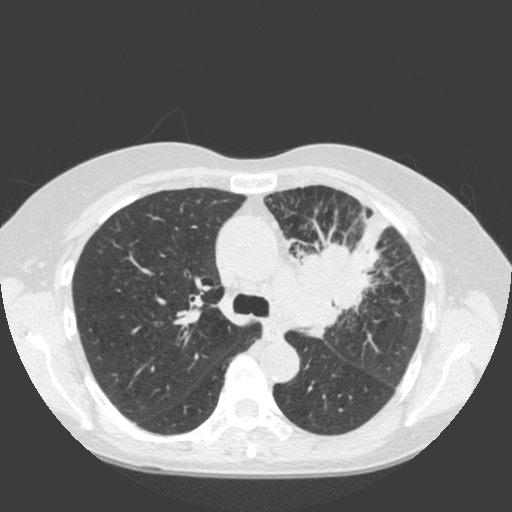
Low-dose screening chest CT, axial slice. First (baseline) screen. Lung window (W 1500 / L -600 HU). 2 mm slice thickness. Standard (soft-tissue) reconstruction kernel (C). 120 kVp. Female, age 66 years at enrolment. Current smoker at enrolment.
- Lesion marked by an expert reader, bounding box [x1, y1, x2, y2] px = [282, 227, 399, 331].
- Reader record for this screening exam (exam-level; its link to the box is not recorded): non-calcified nodule or mass ≥4 mm, left upper lobe, 61 × 45 mm, spiculated (stellate) margins, soft tissue attenuation.
- Official screen result: positive, change unspecified: nodule(s) >= 4 mm or enlarging nodule(s), mass(es), or other non-specific abnormalities suspicious for lung cancer.
- Later outcome: lung cancer diagnosed 19 days after this screen — squamous cell carcinoma, keratinizing, NOS, left upper lobe, left hilum, mediastinum, left main stem bronchus, other location, poorly differentiated (G3), stage IIIB (AJCC 6th edition), 60 mm at pathology.